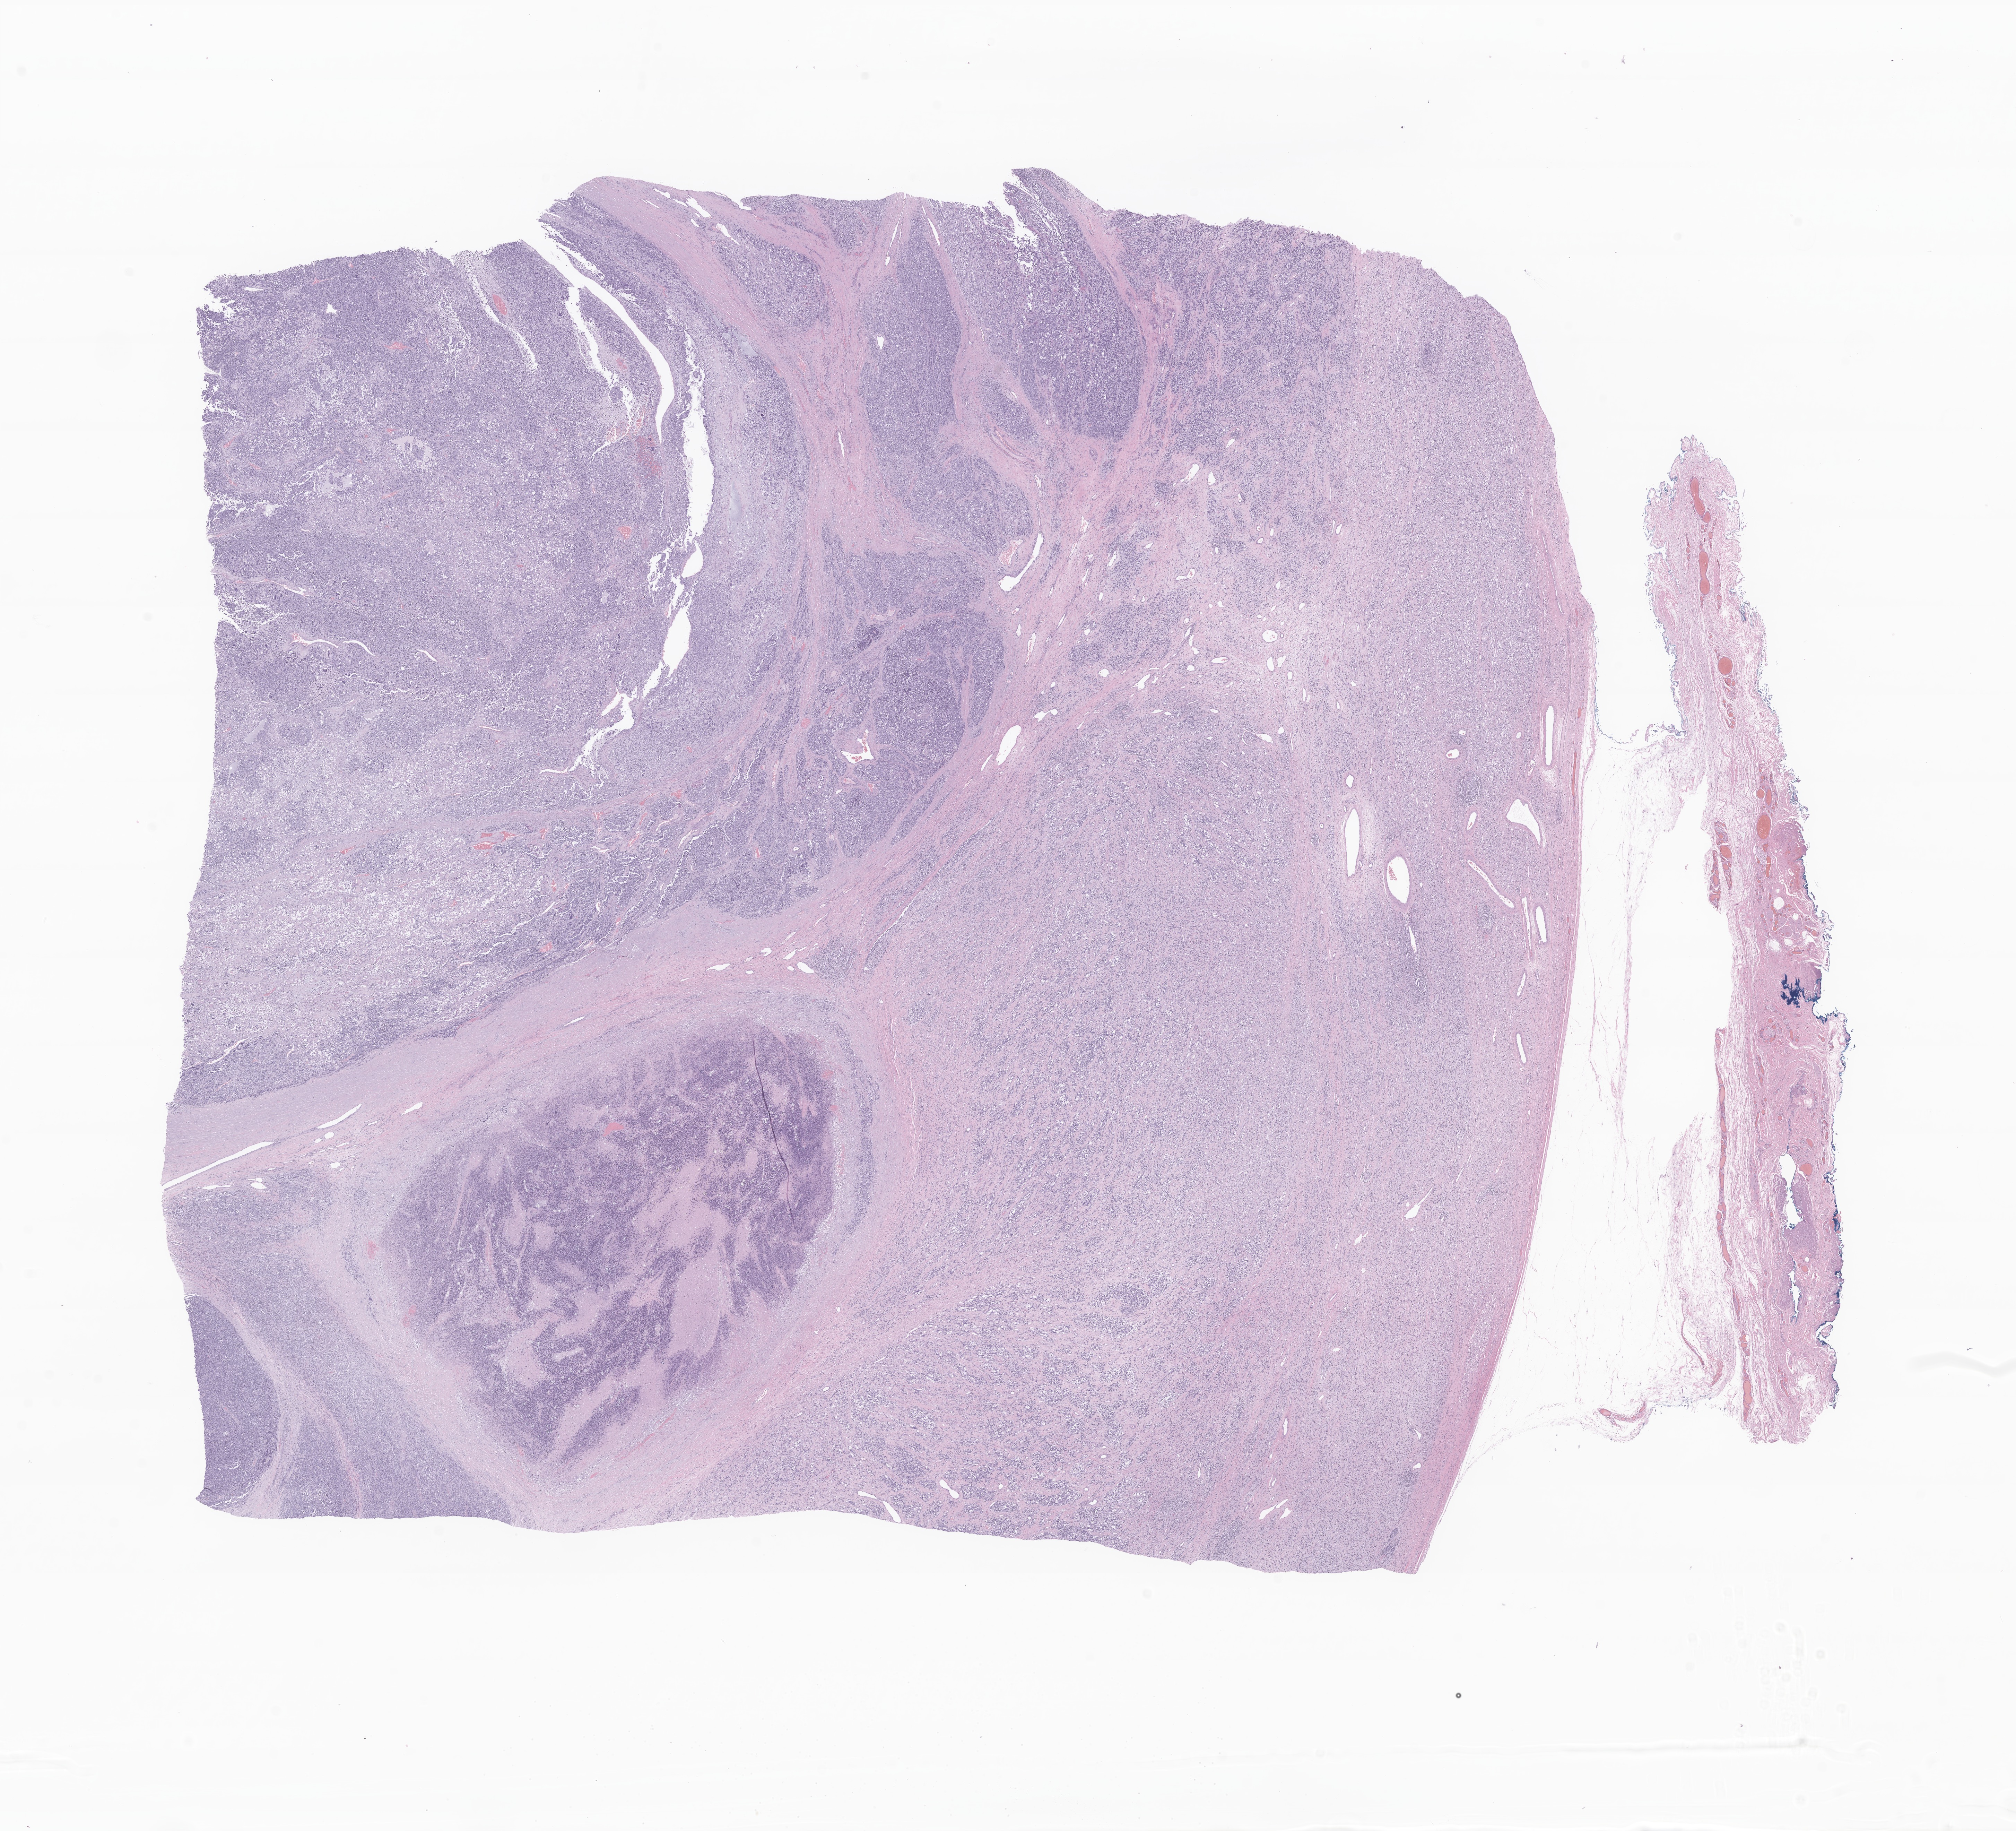
Digitized hematoxylin and eosin (H&E)-stained section of tumor tissue from the testis, shown as a low-resolution overview of the whole scanned area (about 24.5 x 22.3 mm); FFPE section. Patient male; age 99 months.
Diagnosis: Neoplasm, uncertain whether benign or malignant.